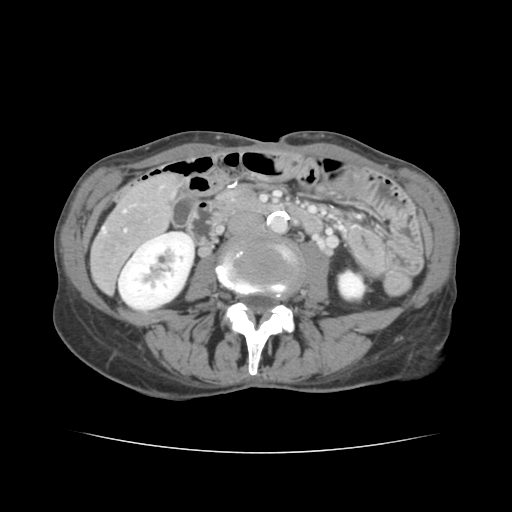
Contrast-enhanced abdominal CT, one axial slice; slice 36 of 136 in the series (ordered by position); intravenous contrast given; soft-tissue window (W 400 / L 40 HU); 512 × 512 image matrix, field of view 319 × 319 mm. Female patient, age 77 years. Case-level facts recorded for this patient, not image findings: diagnosis: colorectal cancer liver metastases, imaged before liver resection; multiple liver metastases: yes; largest metastasis: 3 cm; disease in both lobes: no.
Structures marked on this image (manually delineated by an expert):
- hepatic veins: bounding box <103,210,126,233> (left, top, right, bottom; pixels)
- liver: <92,176,177,290>